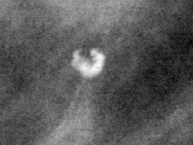
Region of interest cut from a scanned film mammogram (one marked finding), left breast, CC view.
Calcifications, morphology round and regular / lucent center; BI-RADS assessment category 2; benign without callback (not worked up further).